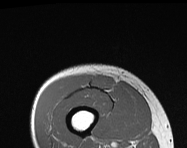
MRI of an extremity soft-tissue mass, one axial slice. Position 31 of 114 along the scan axis. MR volume resampled by the dataset authors to the PET/CT grid (not the native acquisition matrix). 3.27 mm slice thickness. 187 × 148 image matrix, field of view 183 × 145 mm. Male patient. From the clinical record (not read from this slice): histological type: pleiomorphic leiomyosarcoma; grade: intermediate; site of the primary tumour: right thigh.
Outlined on this slice (expert contour drawn on MRI and transferred to this co-registered scan by the dataset authors):
- gross tumour volume including surrounding oedema: bounding box <91,75,115,91> (left, top, right, bottom; pixels)